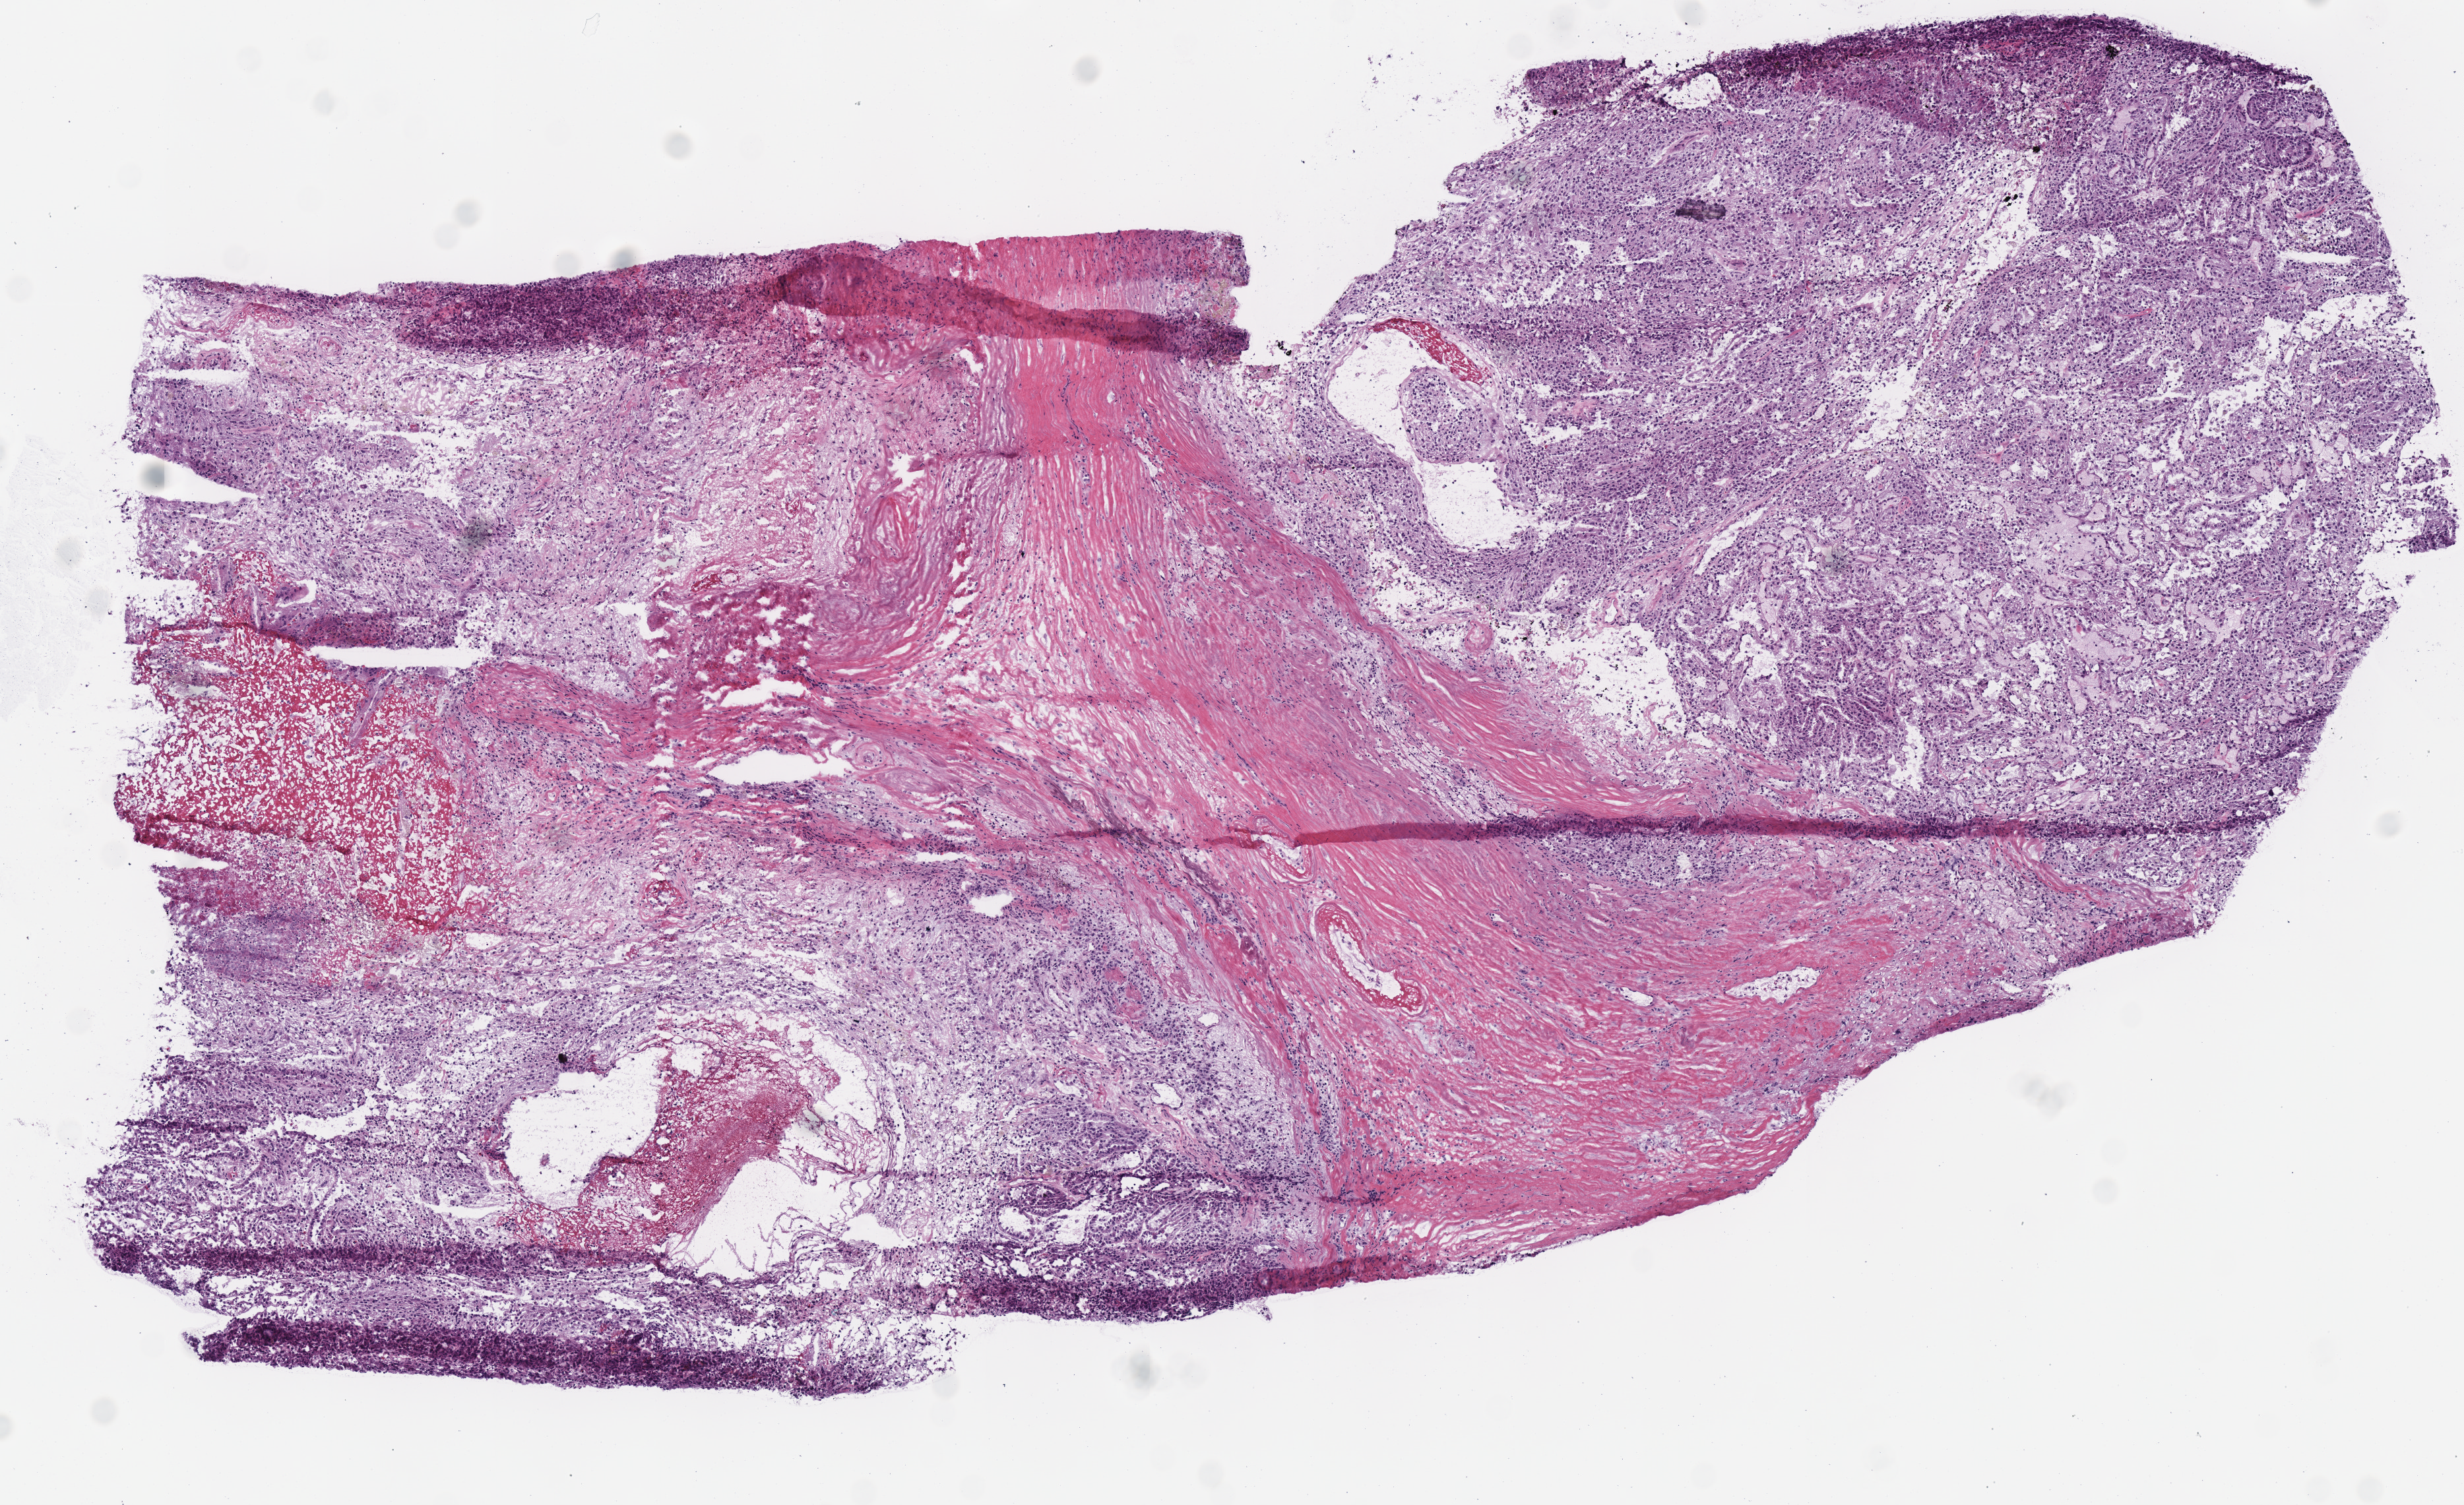
Whole-slide histology image, H&E, low-resolution overview of the scanned area, about 7.3 x 4.5 mm; frozen section; sample: primary tumour, kidney. Patient: female, age at initial diagnosis 48 years. Slide review estimates, as recorded: tumour cells 60%, tumour nuclei 60%, normal cells 0%, stromal cells 32%, necrosis 8%. Infiltration values recorded for this section: lymphocyte infiltration 10%, monocyte infiltration 10%, neutrophil infiltration 10%.
AJCC pathologic stage: I (7th edition). Diagnosis: Papillary adenocarcinoma, NOS. Laterality: right.